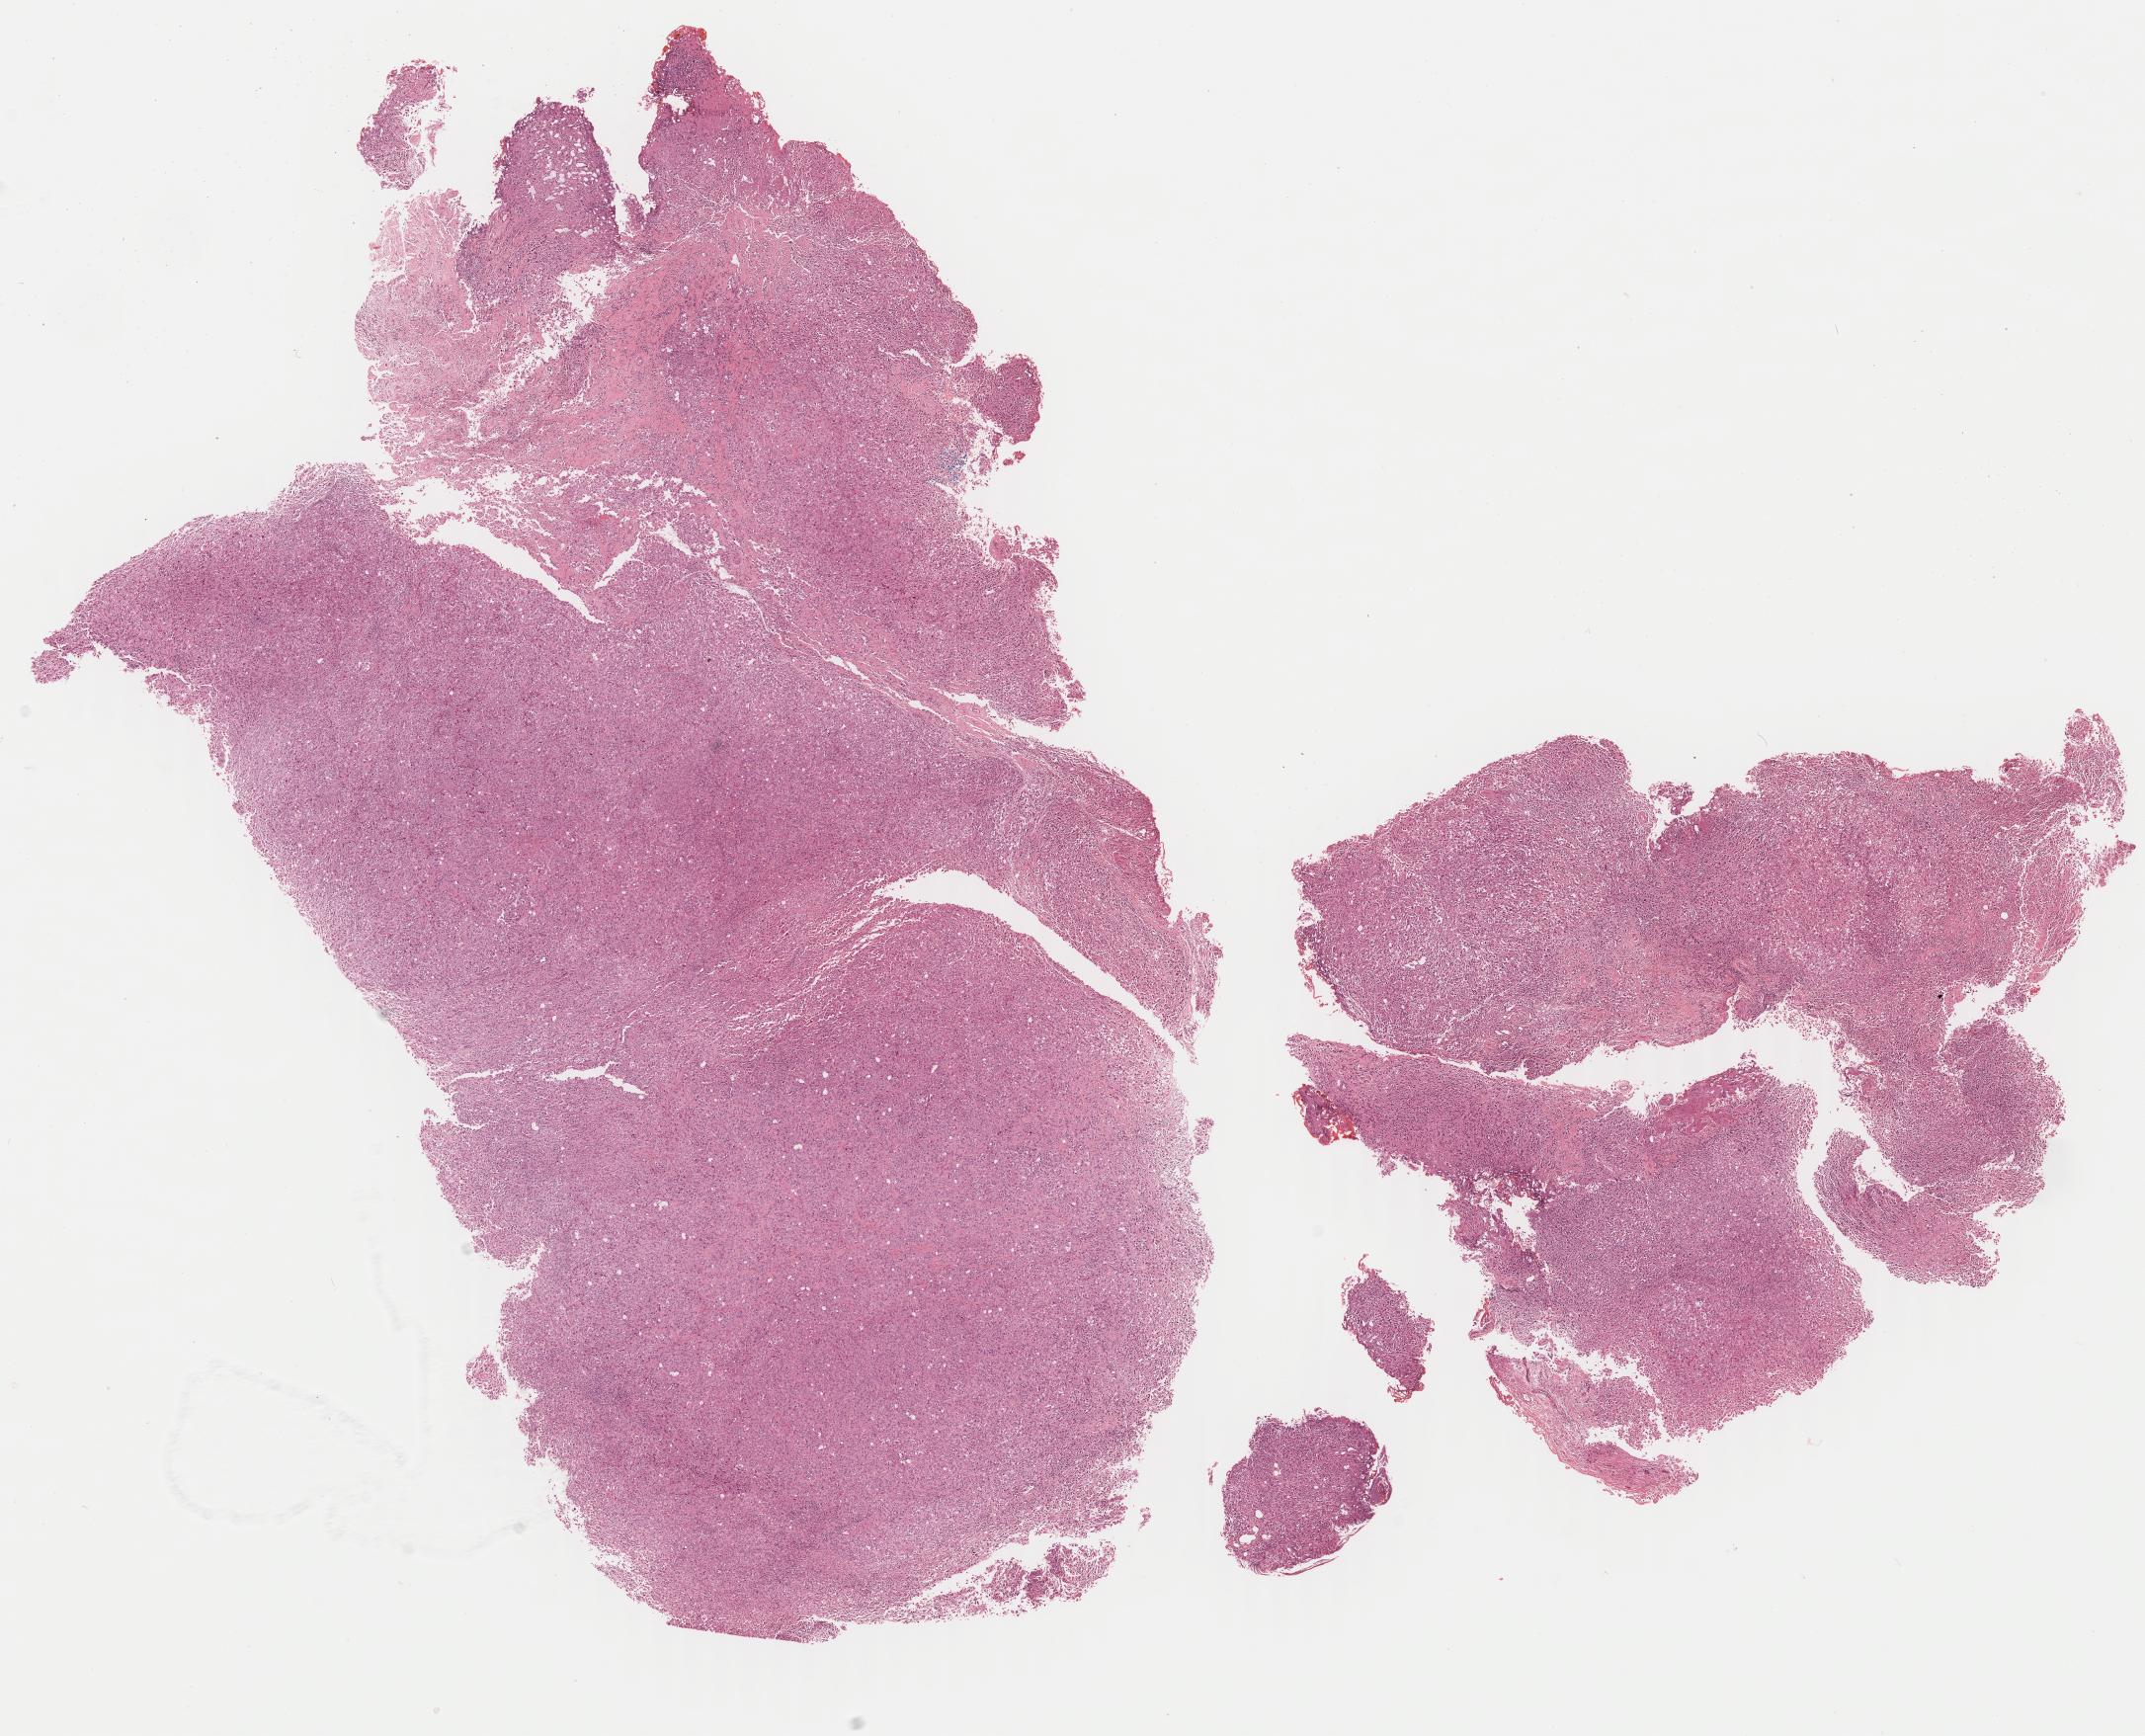
Digitized H&E tissue section (whole slide), a low-resolution overview of the entire scanned area, about 17.2 x 13.9 mm (slide scanned at 40x); FFPE section; primary tumour sample from the mesothelium. Male, age 47 years at initial diagnosis.
AJCC pathologic stage: II (6th edition). Histologic diagnosis: Epithelioid mesothelioma, malignant (pleura, NOS).